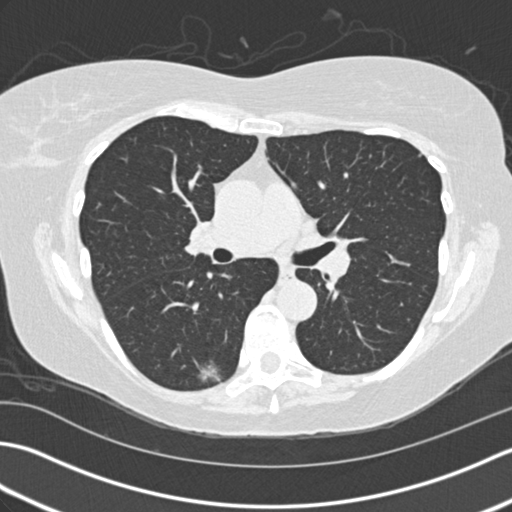
Chest CT (low-dose screening protocol), one axial image. Third screening round (two years after baseline). Lung window (W 1500 / L -600 HU). 2 mm slice thickness. Standard (soft-tissue) reconstruction kernel (B30f). 512 × 512 image matrix. Female participant, aged 60 years at enrolment. Former smoker at enrolment.
Expert reader's lesion annotation, bounding box (x1, y1, x2, y2) in pixels: (187, 349, 236, 390). The screening reader recorded 3 non-calcified nodules or masses ≥4 mm on this exam (right lower lobe, right middle lobe, right middle lobe); which of them this box marks is not recorded. Lung cancer was diagnosed 68 days after this screen: acinar cell carcinoma, right lower lobe, moderately differentiated (G2), stage IA (AJCC 6th edition), 10 mm at pathology.